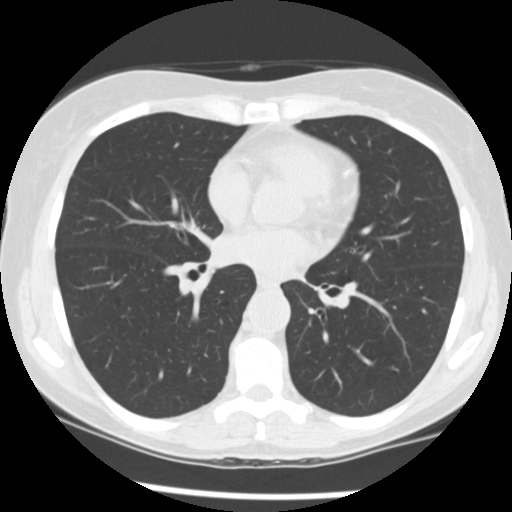
Low-dose screening chest CT, one axial slice. Slice 129 of 241 in the series (ordered by position). Reconstruction kernel STANDARD. 120 kVp. Lung window (W 1500 / L -600 HU). 512 × 512 image matrix, field of view 320 × 320 mm.
Structures marked on this image (expert manual segmentation):
- lesion 1 (tumor, upper lobe of right lung): box from (x=72, y=173) to (x=74, y=176) px